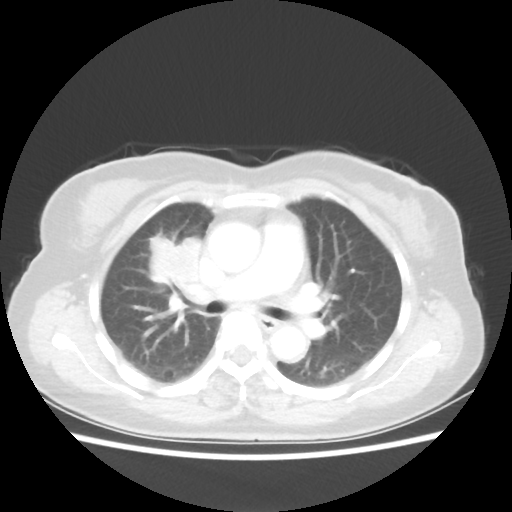
Chest CT, one axial slice; reconstruction kernel STANDARD; 80 kVp; lung window (W 1500 / L -600 HU); 512 × 512 image matrix, field of view 337 × 337 mm. Patient: female, 62 years. From the clinical record (not read from this slice): clinical TNM (as recorded): T4 N3 M0.
Structures marked on this image (rectangle marked by the reading radiologist):
- lung tumour (recorded histology: squamous cell carcinoma): box from (x=133, y=221) to (x=209, y=302) px